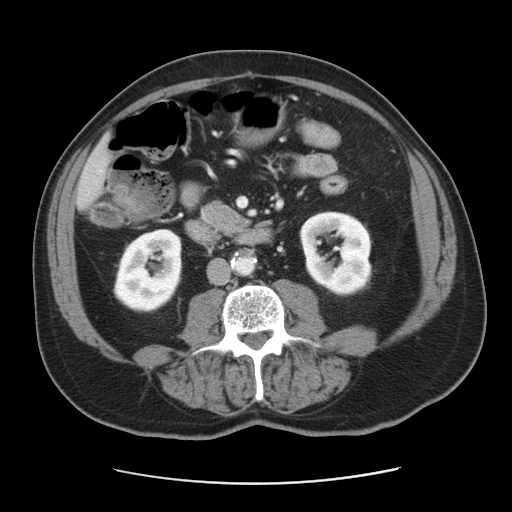
Contrast-enhanced abdominal CT, one axial slice; position 11 of 42 along the scan axis; reconstruction kernel STANDARD; intravenous contrast given; soft-tissue window (W 400 / L 40 HU); 5 mm slice thickness; 512 × 512 image matrix, field of view 370 × 370 mm. Male patient, age 73 years. From the clinical record (not read from this slice): diagnosis: colorectal cancer liver metastases, imaged before liver resection; multiple liver metastases: yes; largest metastasis: 0.5 cm; disease in both lobes: no.
Outlined on this slice (outlined manually by an expert reader):
- liver: box from (x=78, y=145) to (x=106, y=205) px